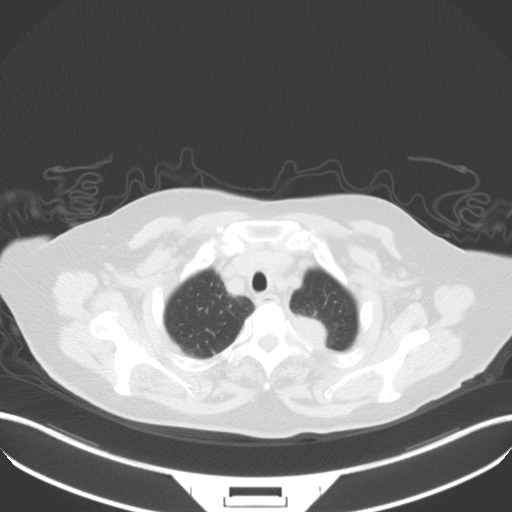
Chest CT, one axial slice; position 43 of 50 along the scan axis; reconstruction kernel B31f; lung window (W 1500 / L -600 HU); 5 mm slice thickness; 512 × 512 image matrix, field of view 400 × 400 mm. Female patient, age 81 years. Case-level facts recorded for this patient, not image findings: clinical TNM (as recorded): T2a N0 M0.
Structures marked on this image (rectangle marked by the reading radiologist):
- lung tumour (recorded histology: adenocarcinoma): bounding box <293,309,341,355> (left, top, right, bottom; pixels)